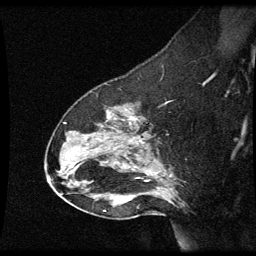
Breast MRI (dynamic contrast-enhanced), one sagittal slice; position 40 of 60 along the scan axis; dynamic contrast-enhanced series, image 2 of 3 at this slice position (ordered by acquisition); 1.5 T; TE 4.2 ms, TR 8.9 ms; 2 mm slice thickness; 256 × 256 image matrix, field of view 200 × 200 mm. Female patient, age 49 years. From the clinical record (not read from this slice): setting: breast cancer imaged before/during neoadjuvant chemotherapy; receptor status: HR-positive, HER2-negative.
Annotated regions visible in this slice (semi-automatically segmented with operator editing):
- analysis volume of interest (the breast-tissue region the enhancement analysis was run in; not a lesion): bounding box (x1, y1, x2, y2) in pixels: (46, 92, 177, 205)
- tumour enhancement mask (voxels above the 70 % enhancement threshold inside the analysis volume of interest): (132, 118, 145, 143)